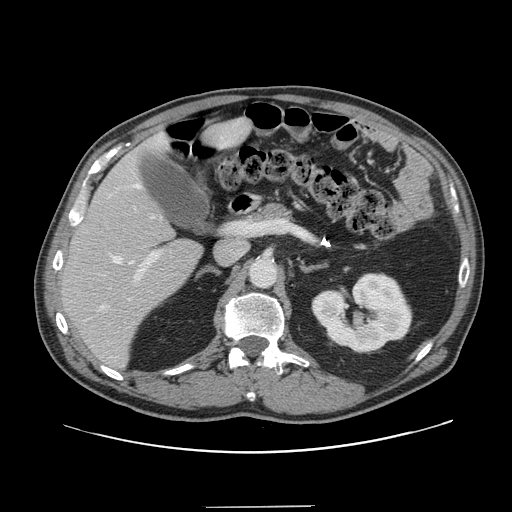
Contrast-enhanced abdominal CT, one axial slice; position 82 of 139 along the scan axis; 120 kVp; intravenous contrast given; soft-tissue window (W 400 / L 40 HU); 512 × 512 image matrix, field of view 397 × 397 mm. Male patient, age 64 years. Case-level facts recorded for this patient, not image findings: diagnosis: colorectal cancer liver metastases, imaged before liver resection; multiple liver metastases: yes; largest metastasis: 3.5 cm; disease in both lobes: yes.
Structures marked on this image (expert manual segmentation):
- hepatic veins: bounding box (x1, y1, x2, y2) in pixels: (100, 184, 161, 310)
- liver: (62, 121, 247, 368)
- planned liver remnant (the part of the liver to remain after resection): (62, 122, 246, 367)
- portal vein (with intrahepatic branches): (135, 251, 161, 281)